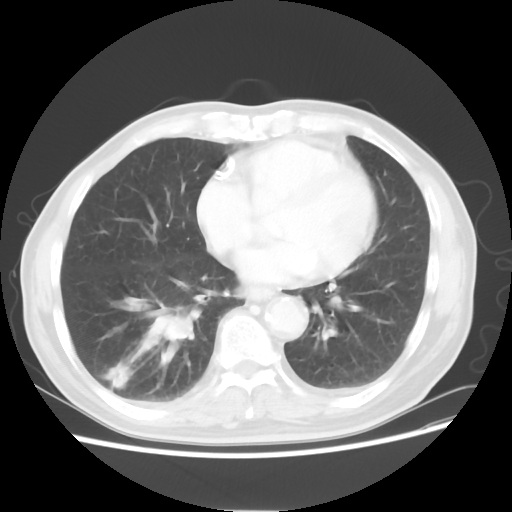
Chest CT, one axial slice; slice 22 of 58 in the series (ordered by position); reconstruction kernel STANDARD; 120 kVp; lung window (W 1500 / L -600 HU); 5 mm slice thickness; 512 × 512 image matrix, field of view 360 × 360 mm. Male patient, age 74 years. From the clinical record (not read from this slice): clinical TNM (as recorded): T1c N1 M1.
Structures marked on this image (rectangle marked by the reading radiologist):
- lung tumour (recorded histology: adenocarcinoma): box from (x=125, y=286) to (x=206, y=367) px